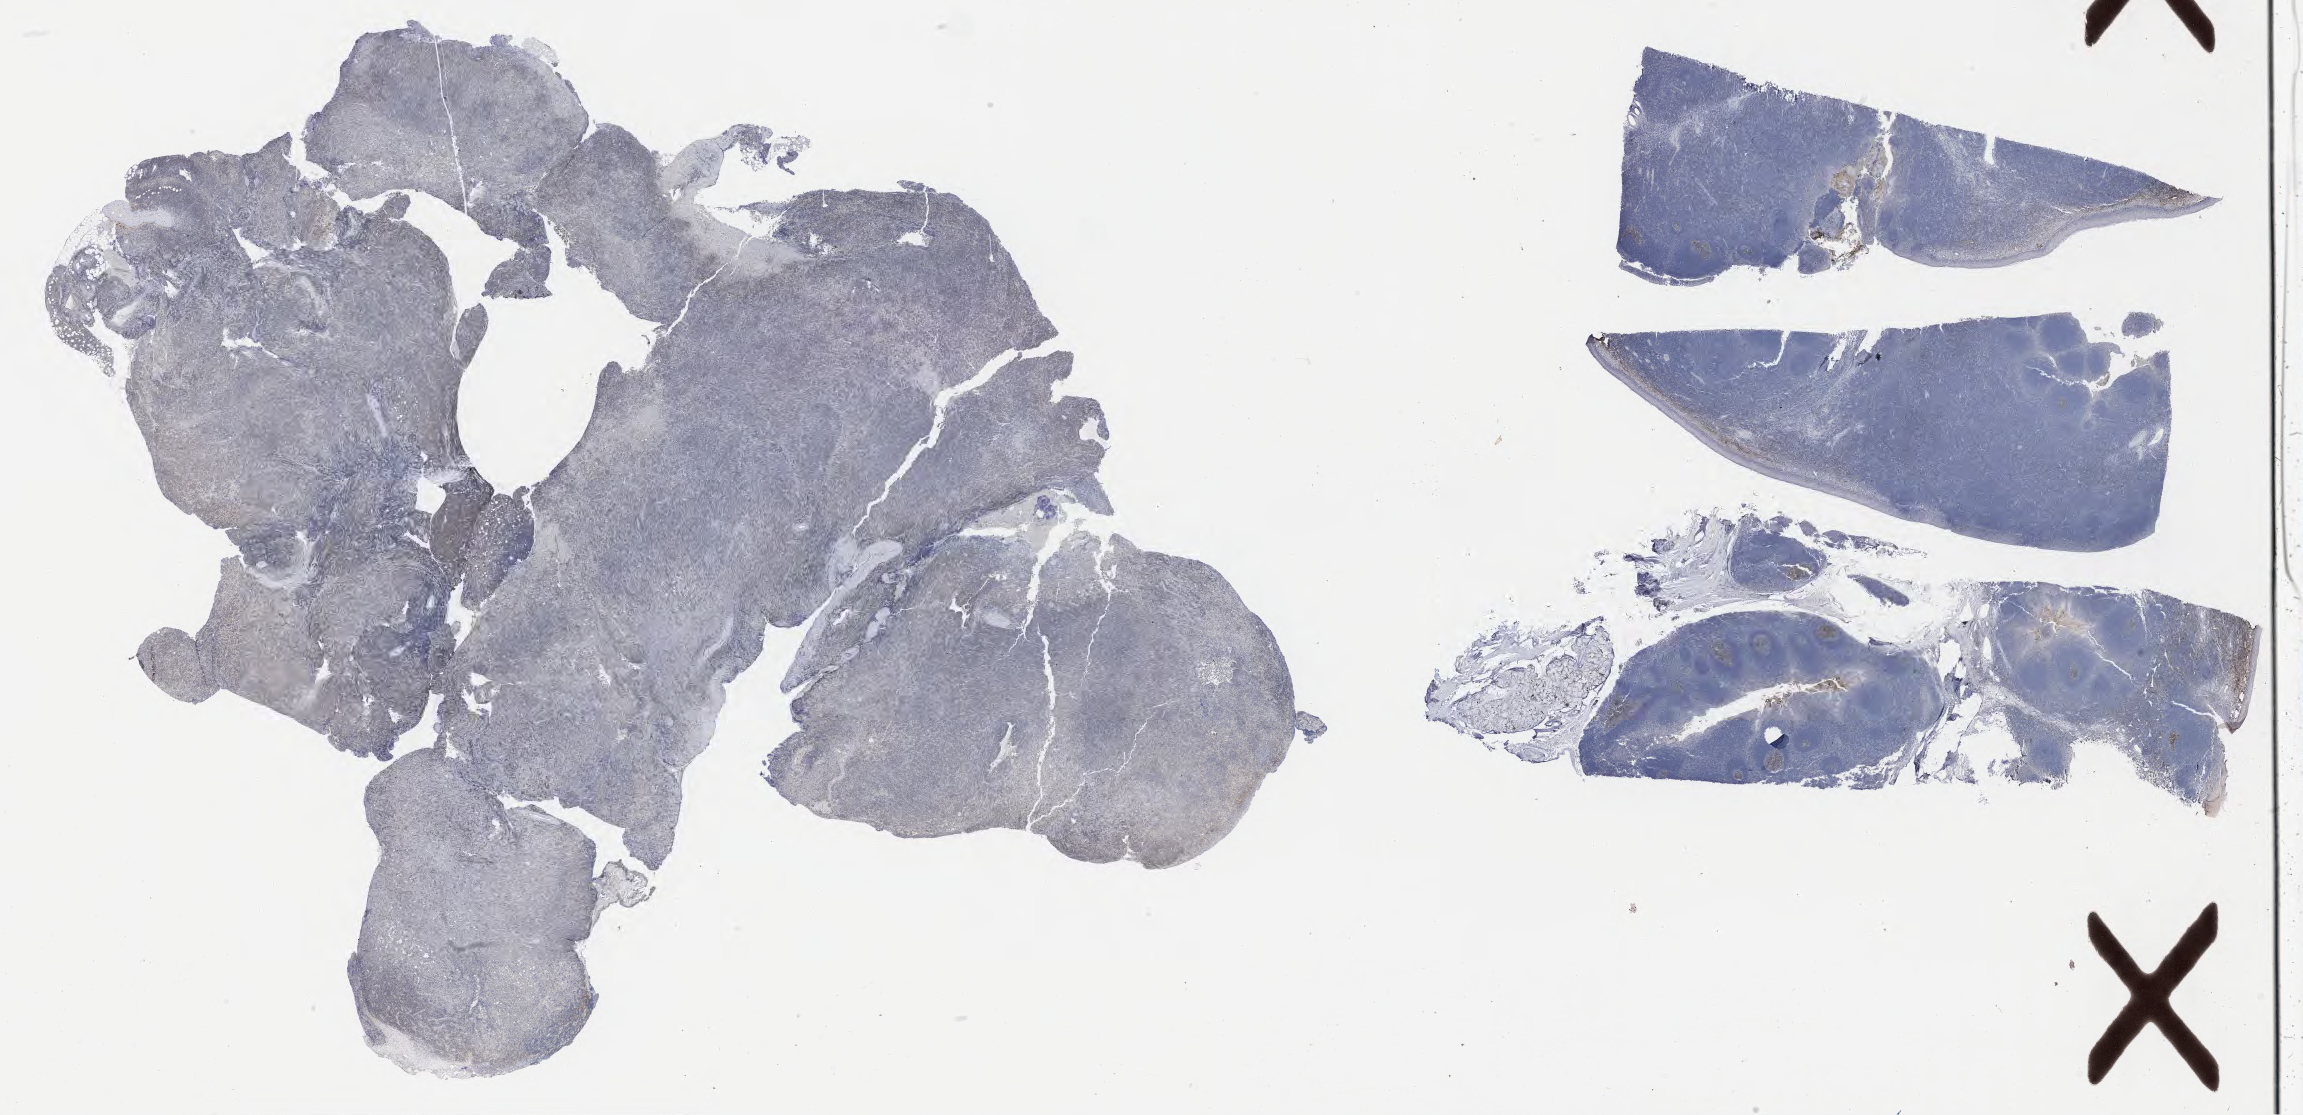
Whole-slide image, immunohistochemical stain for CD10 — shown as a low-resolution overview of the whole scanned area (about 37.2 x 18.0 mm); specimen: tumor tissue; anatomic site: soft tissue of abdomen. Female, age 8 years at initial diagnosis.
Histologic diagnosis: Burkitt lymphoma, NOS.